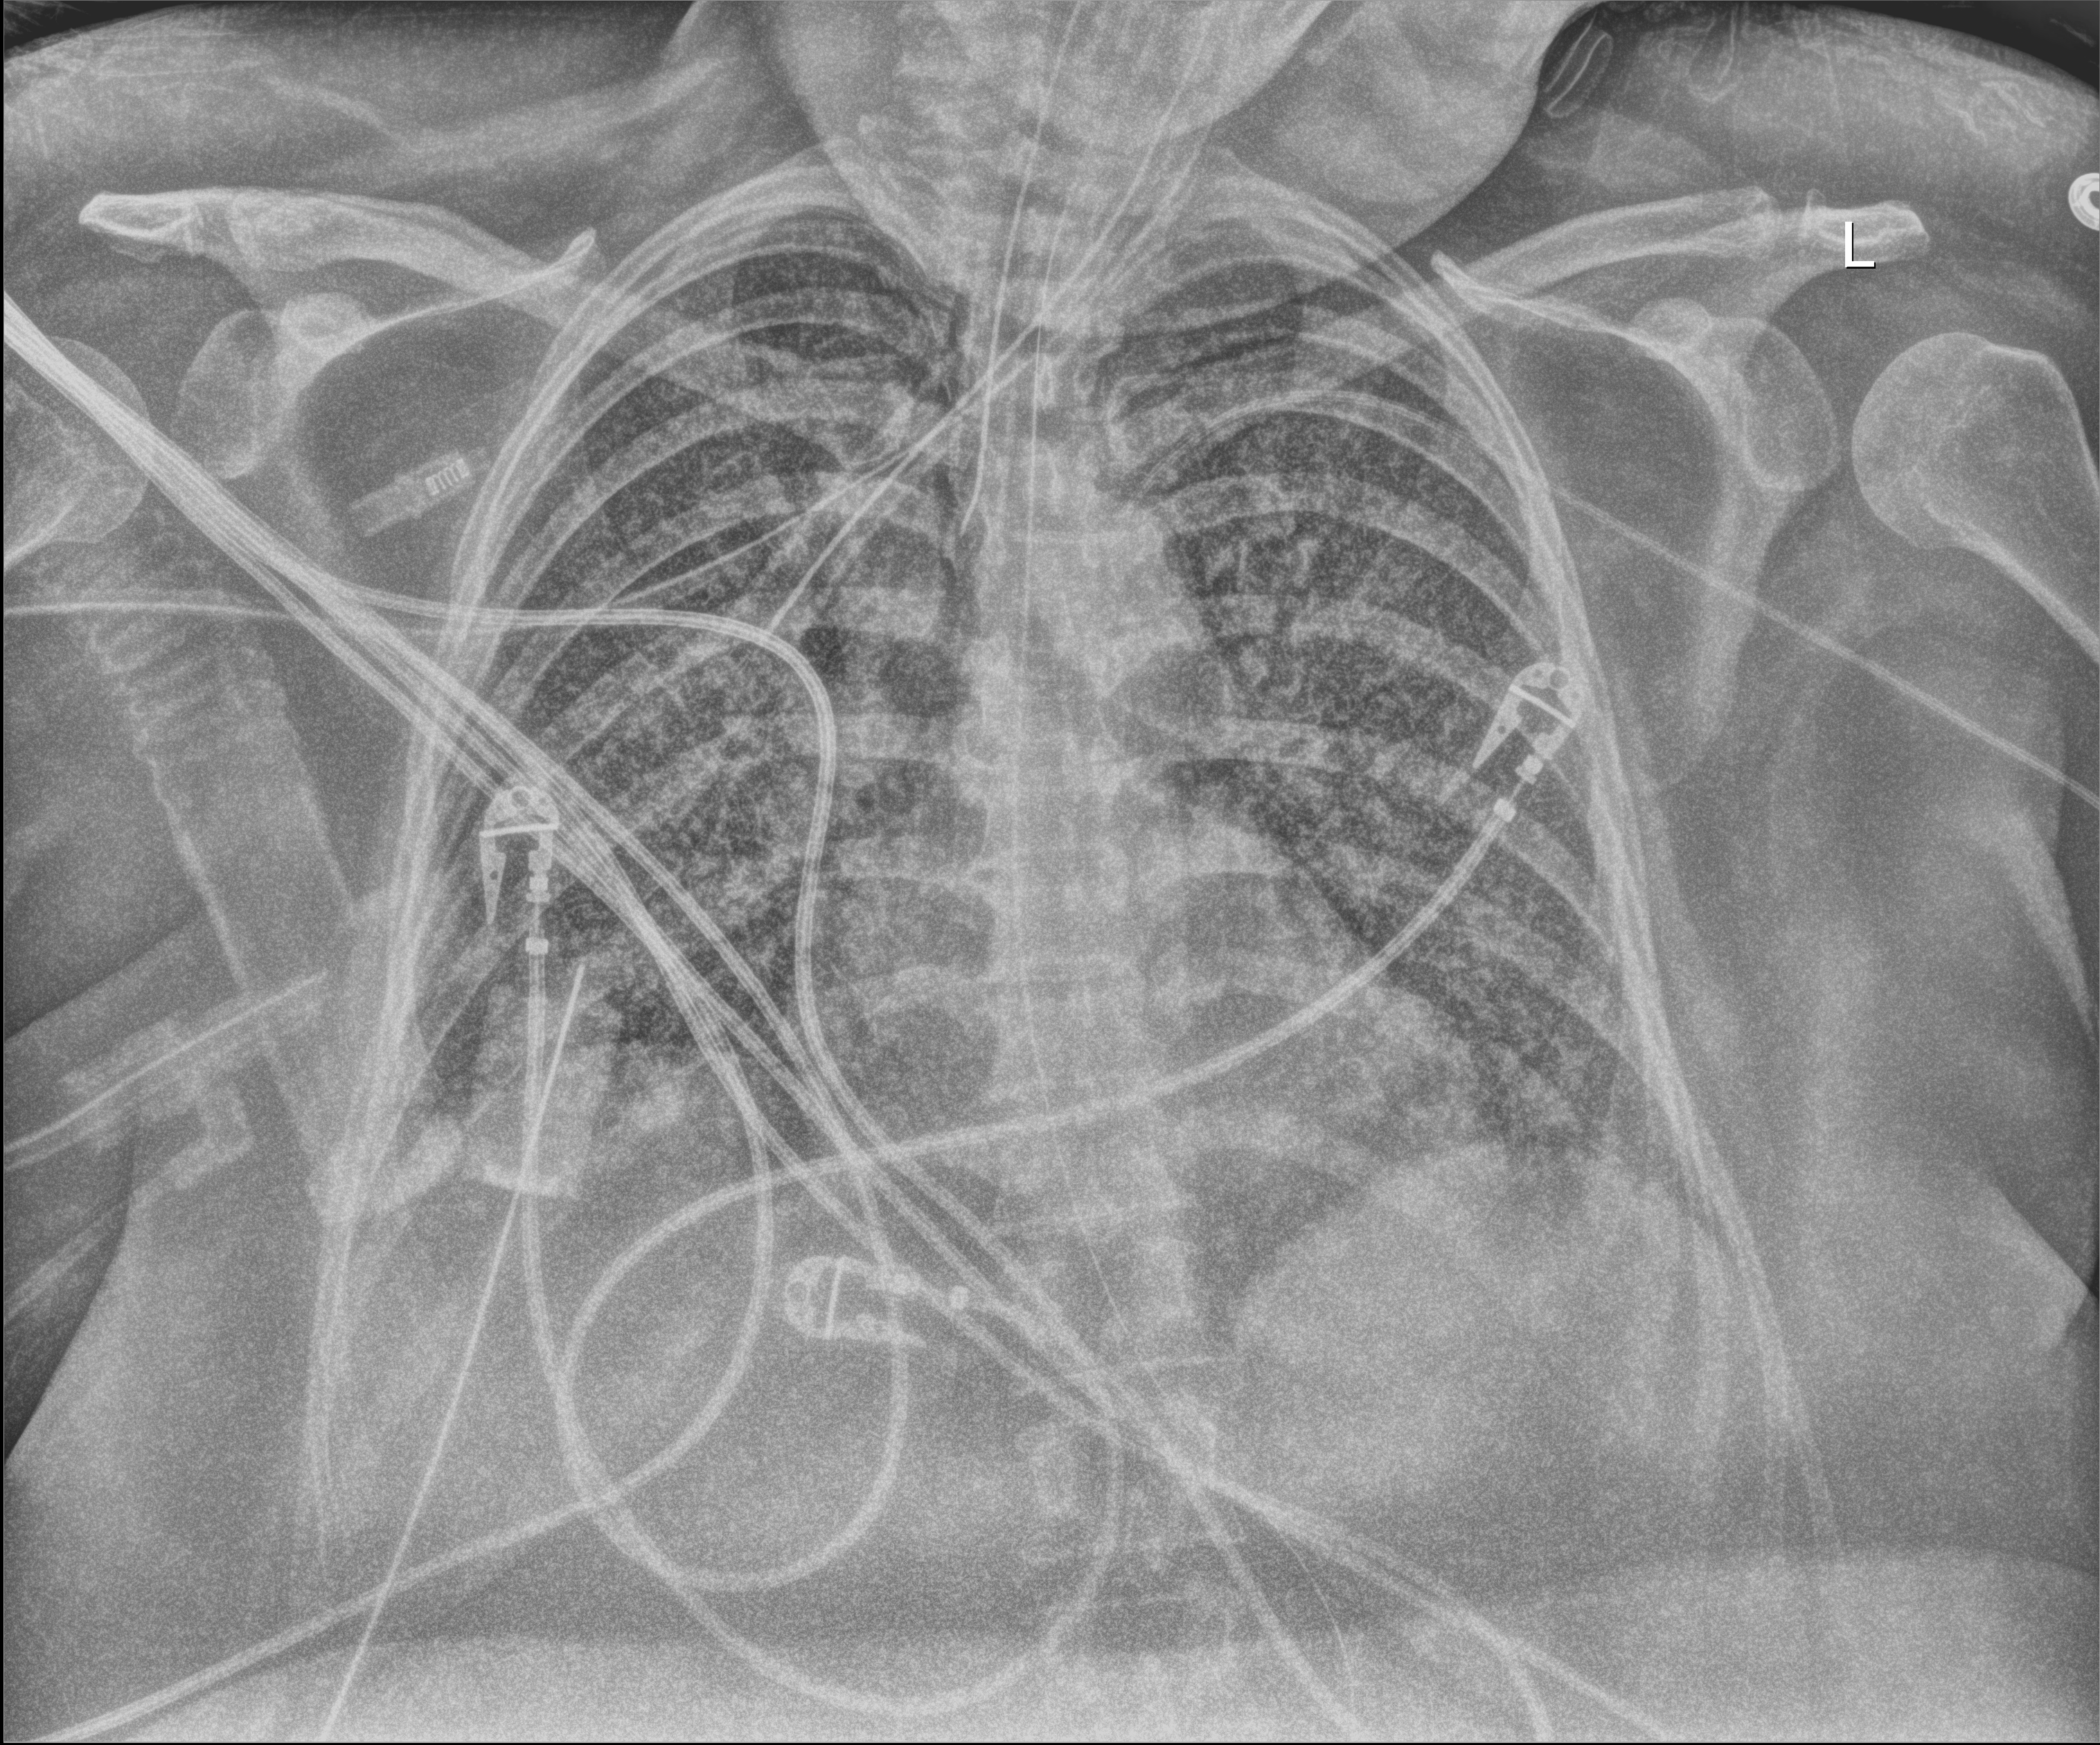
Bedside chest radiograph (digital radiography); anteroposterior (AP) projection. Patient hospitalised with COVID-19; female, aged 18–59 years.
Admission-level facts for this patient (not findings on this image; timing relative to this image not recorded): mechanically ventilated during this hospital stay: yes.